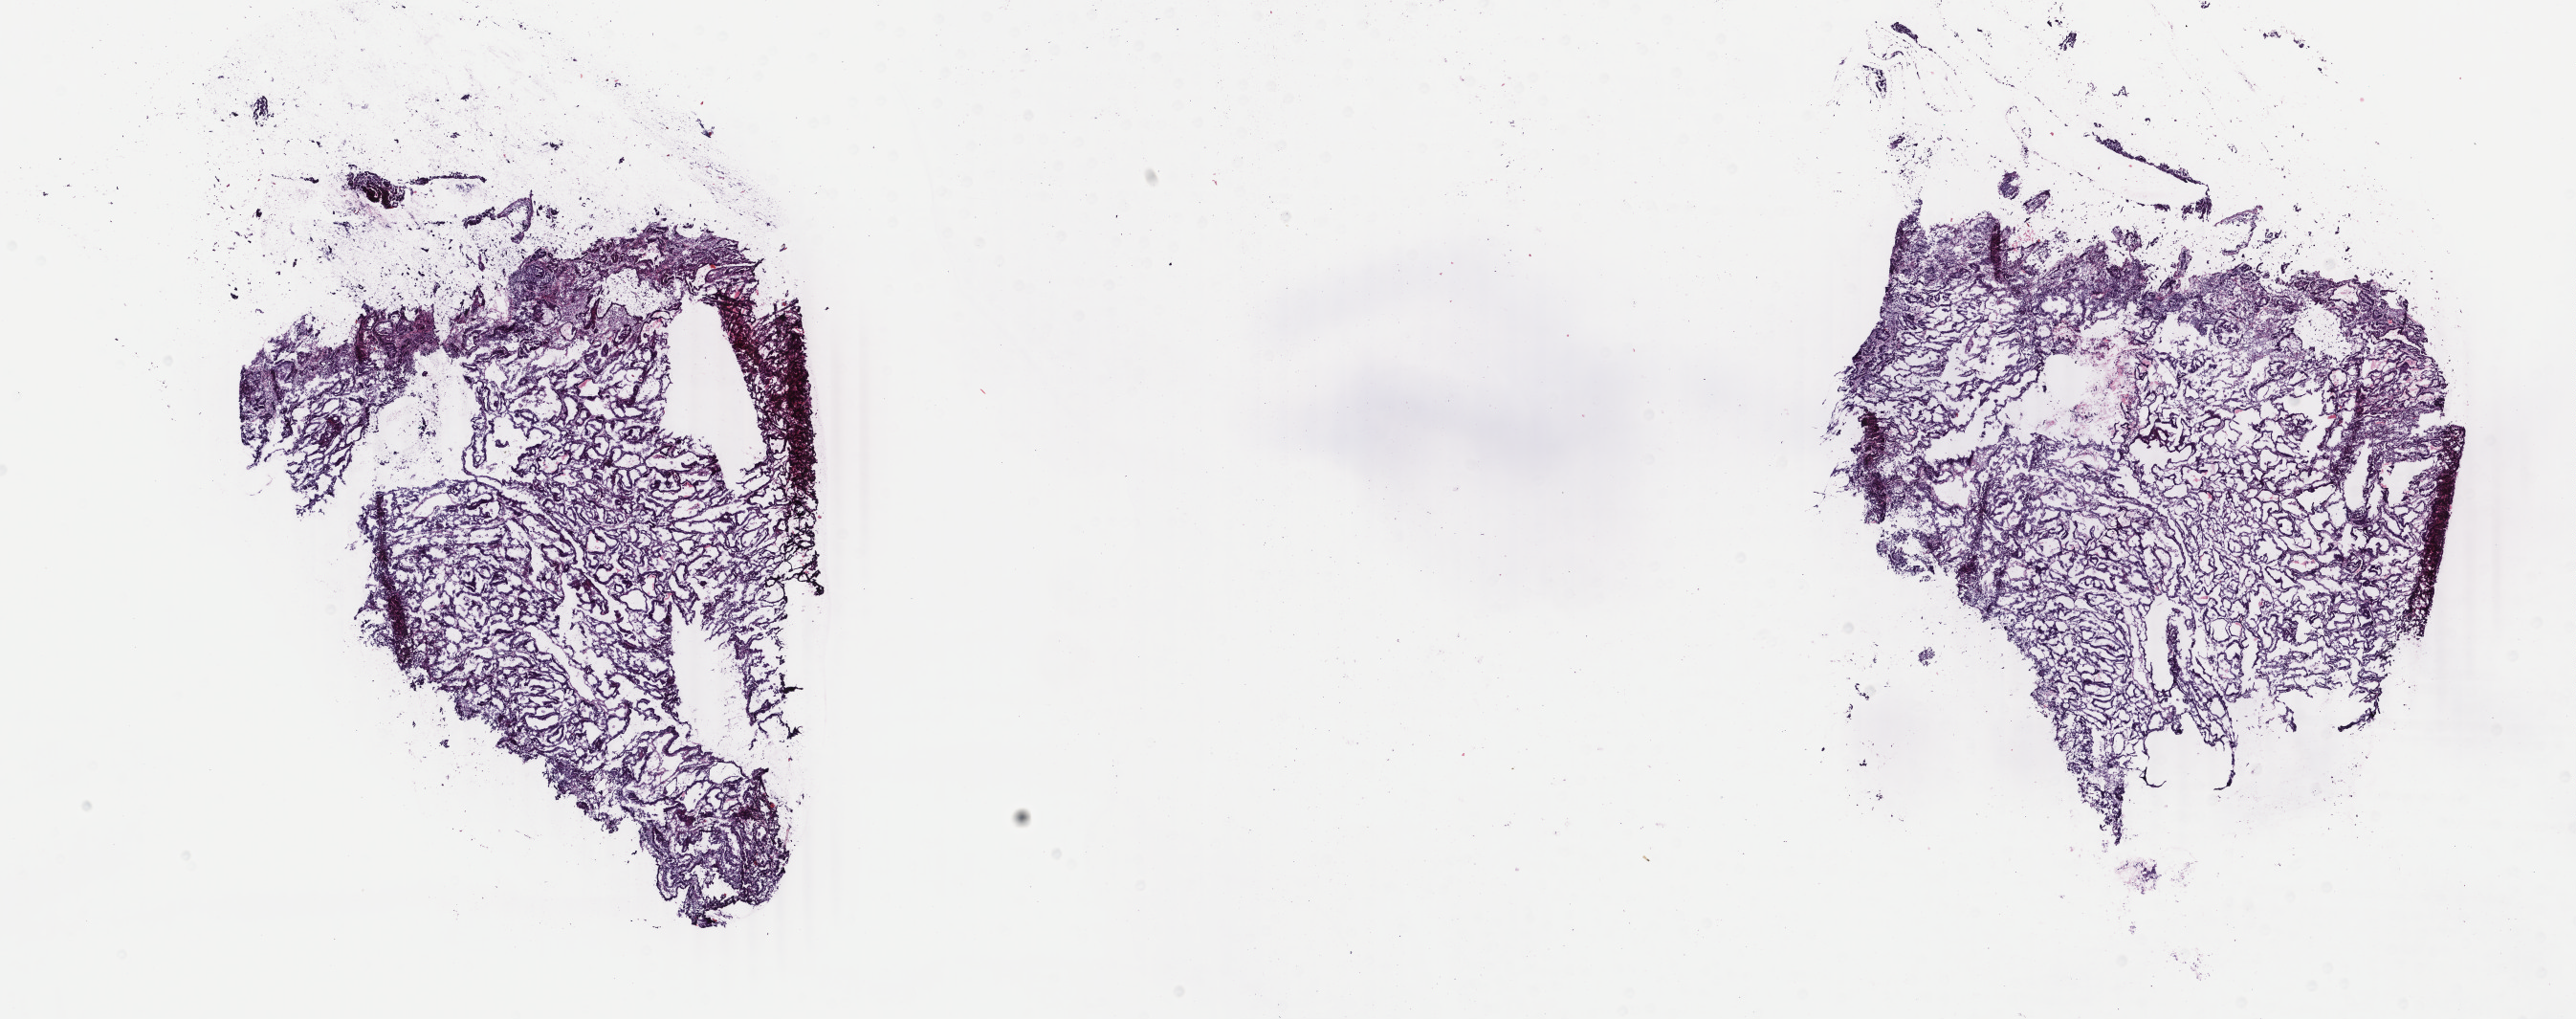
Whole-slide histology image, H&E-stained — whole scanned area (about 21.4 x 8.5 mm, slide scanned at 40x) shown as a low-resolution overview, frozen section from the top of the tissue portion, sample: primary tumour, uterus. Patient: female, age at initial diagnosis 76 years. Histologic grade: G1 (well differentiated). Pathologist review of this section (percent, as recorded): tumour cells 95%, tumour nuclei 85%, normal cells 5%, stromal cells 0%, necrosis 0%. Inflammatory infiltration, as recorded: lymphocyte infiltration 0%, monocyte infiltration 0%, neutrophil infiltration 0%.
• diagnosis: Endometrioid adenocarcinoma, NOS (endometrium)
• FIGO stage: IA